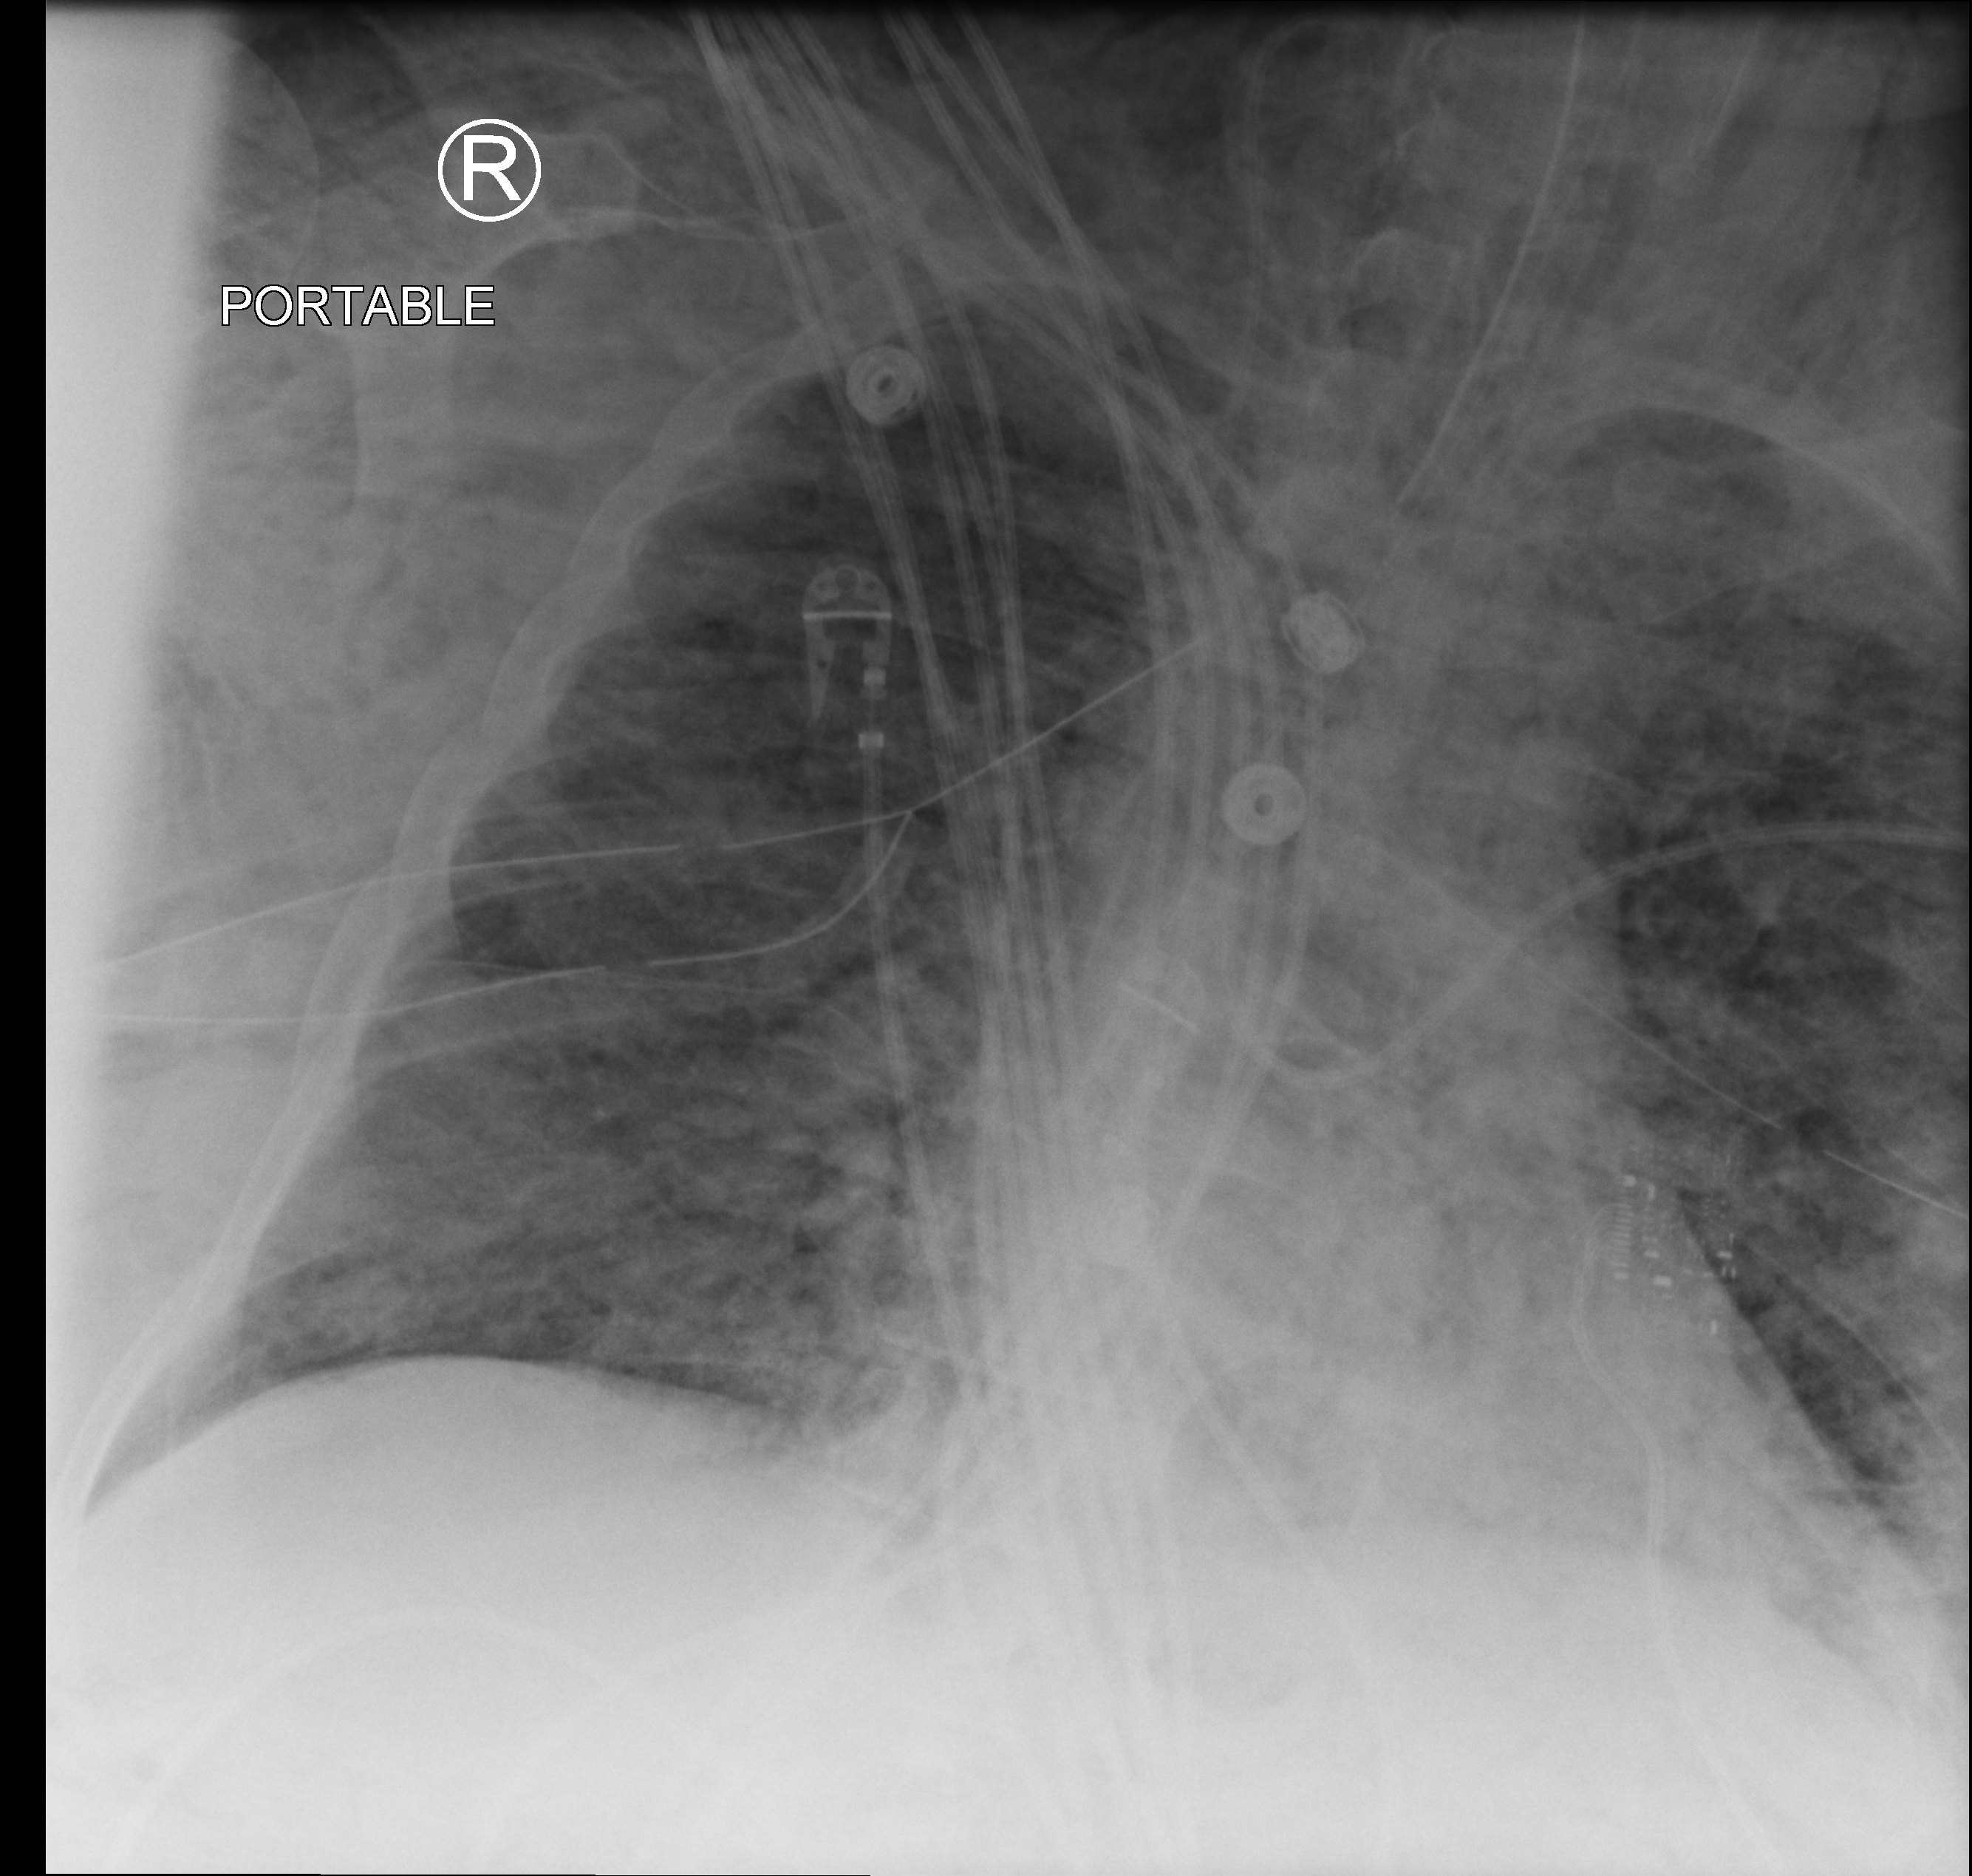
Bedside chest radiograph (computed radiography); anteroposterior (AP) projection. Patient hospitalised with COVID-19, aged 18–59 years.
From the hospital-stay record, not from the radiograph (when in the stay this image was taken is not recorded): admitted to intensive care during this hospital stay: yes; mechanically ventilated during this hospital stay: yes.